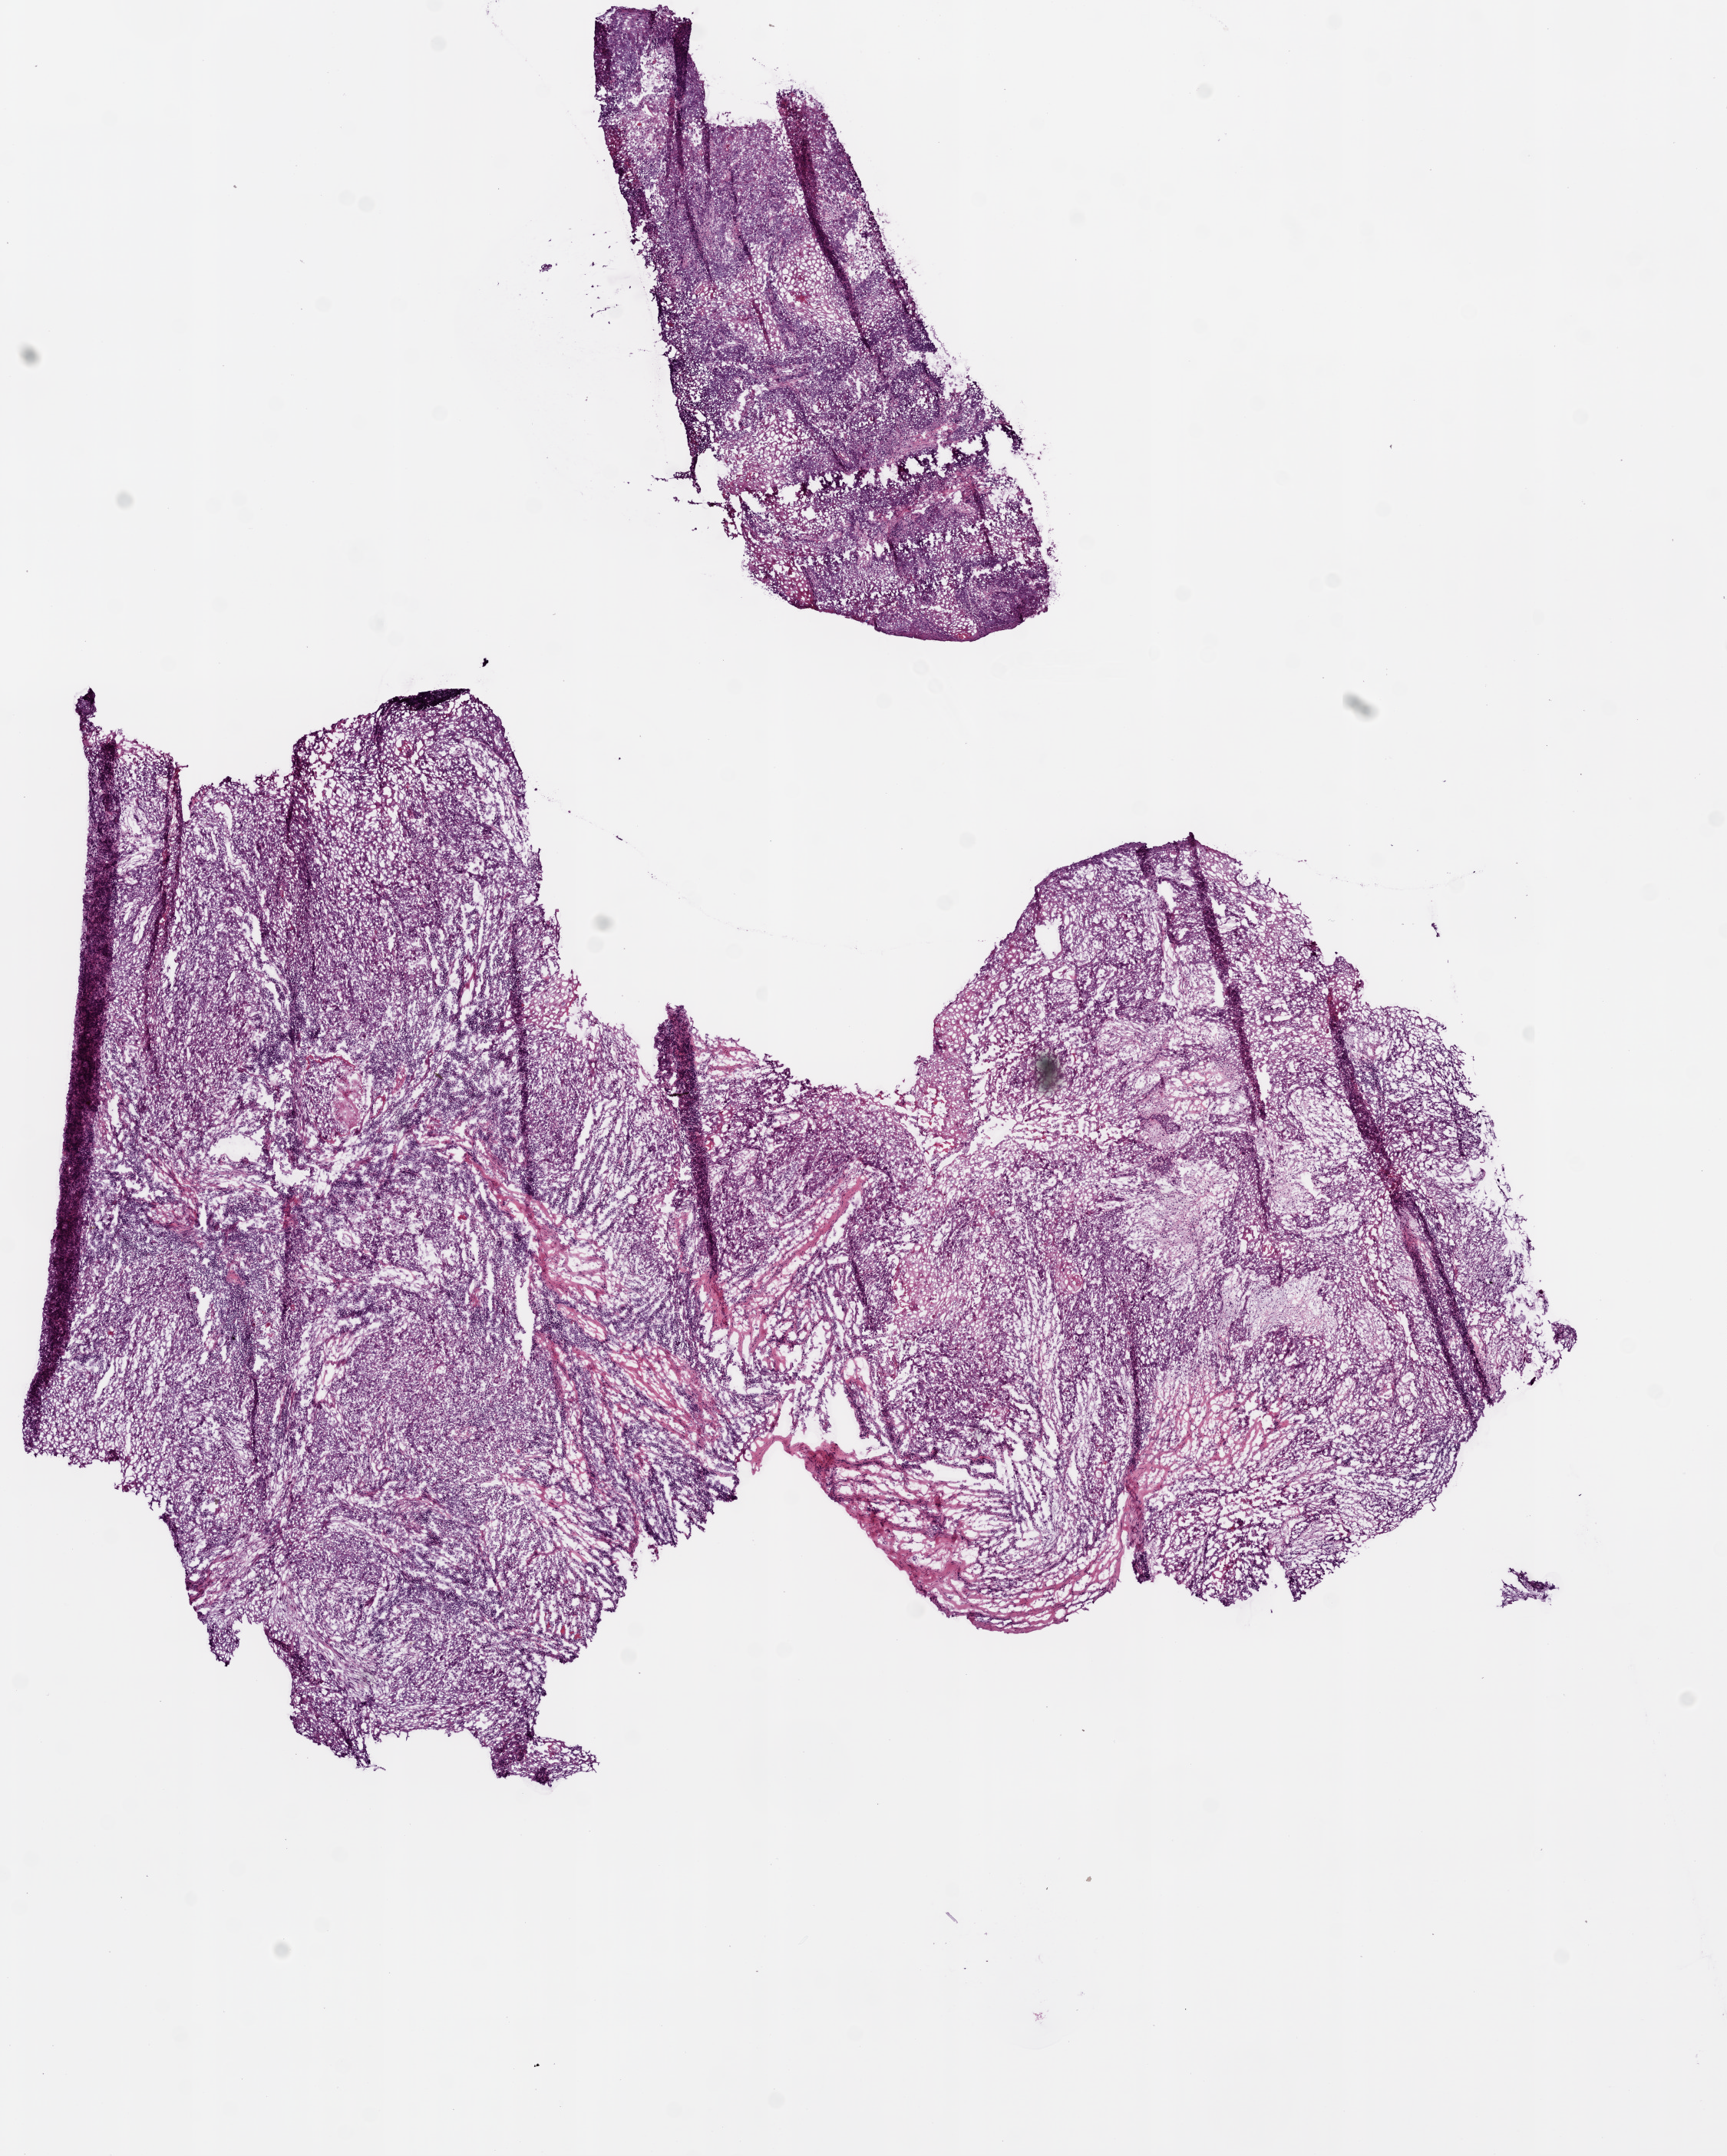
Digitized Hematoxylin and eosin (H&E) stained tissue section (whole slide) — whole scanned area (about 9.0 x 11.3 mm, slide scanned at 20x) shown as a low-resolution overview, frozen section, primary tumour sample from the head and neck. Male patient; age at initial diagnosis 67 years. Histologic grade: G2 (moderately differentiated). Pathologist review of this section (percent, as recorded): tumour cells 87%, tumour nuclei 70%, normal cells 0%, stromal cells 10%, necrosis 3%.
AJCC pathologic stage: IVA. Pathologic diagnosis: Squamous cell carcinoma, NOS (larynx, NOS).